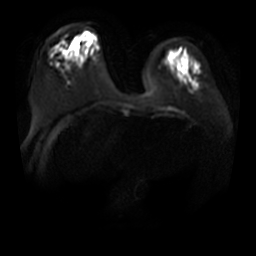
Breast MRI, one axial slice. Slice 12 of 36 in the series (ordered by position). Diffusion-weighted series; image 2 of 4 stored at this slice position (different b-values; order by instance number). 3 T. 5 mm slice thickness. 256 × 256 image matrix, field of view 380 × 380 mm. Female patient.
Structures marked on this image (manually delineated by an expert):
- tumour on diffusion-weighted imaging: bounding box (x1, y1, x2, y2) in pixels: (72, 42, 77, 49)